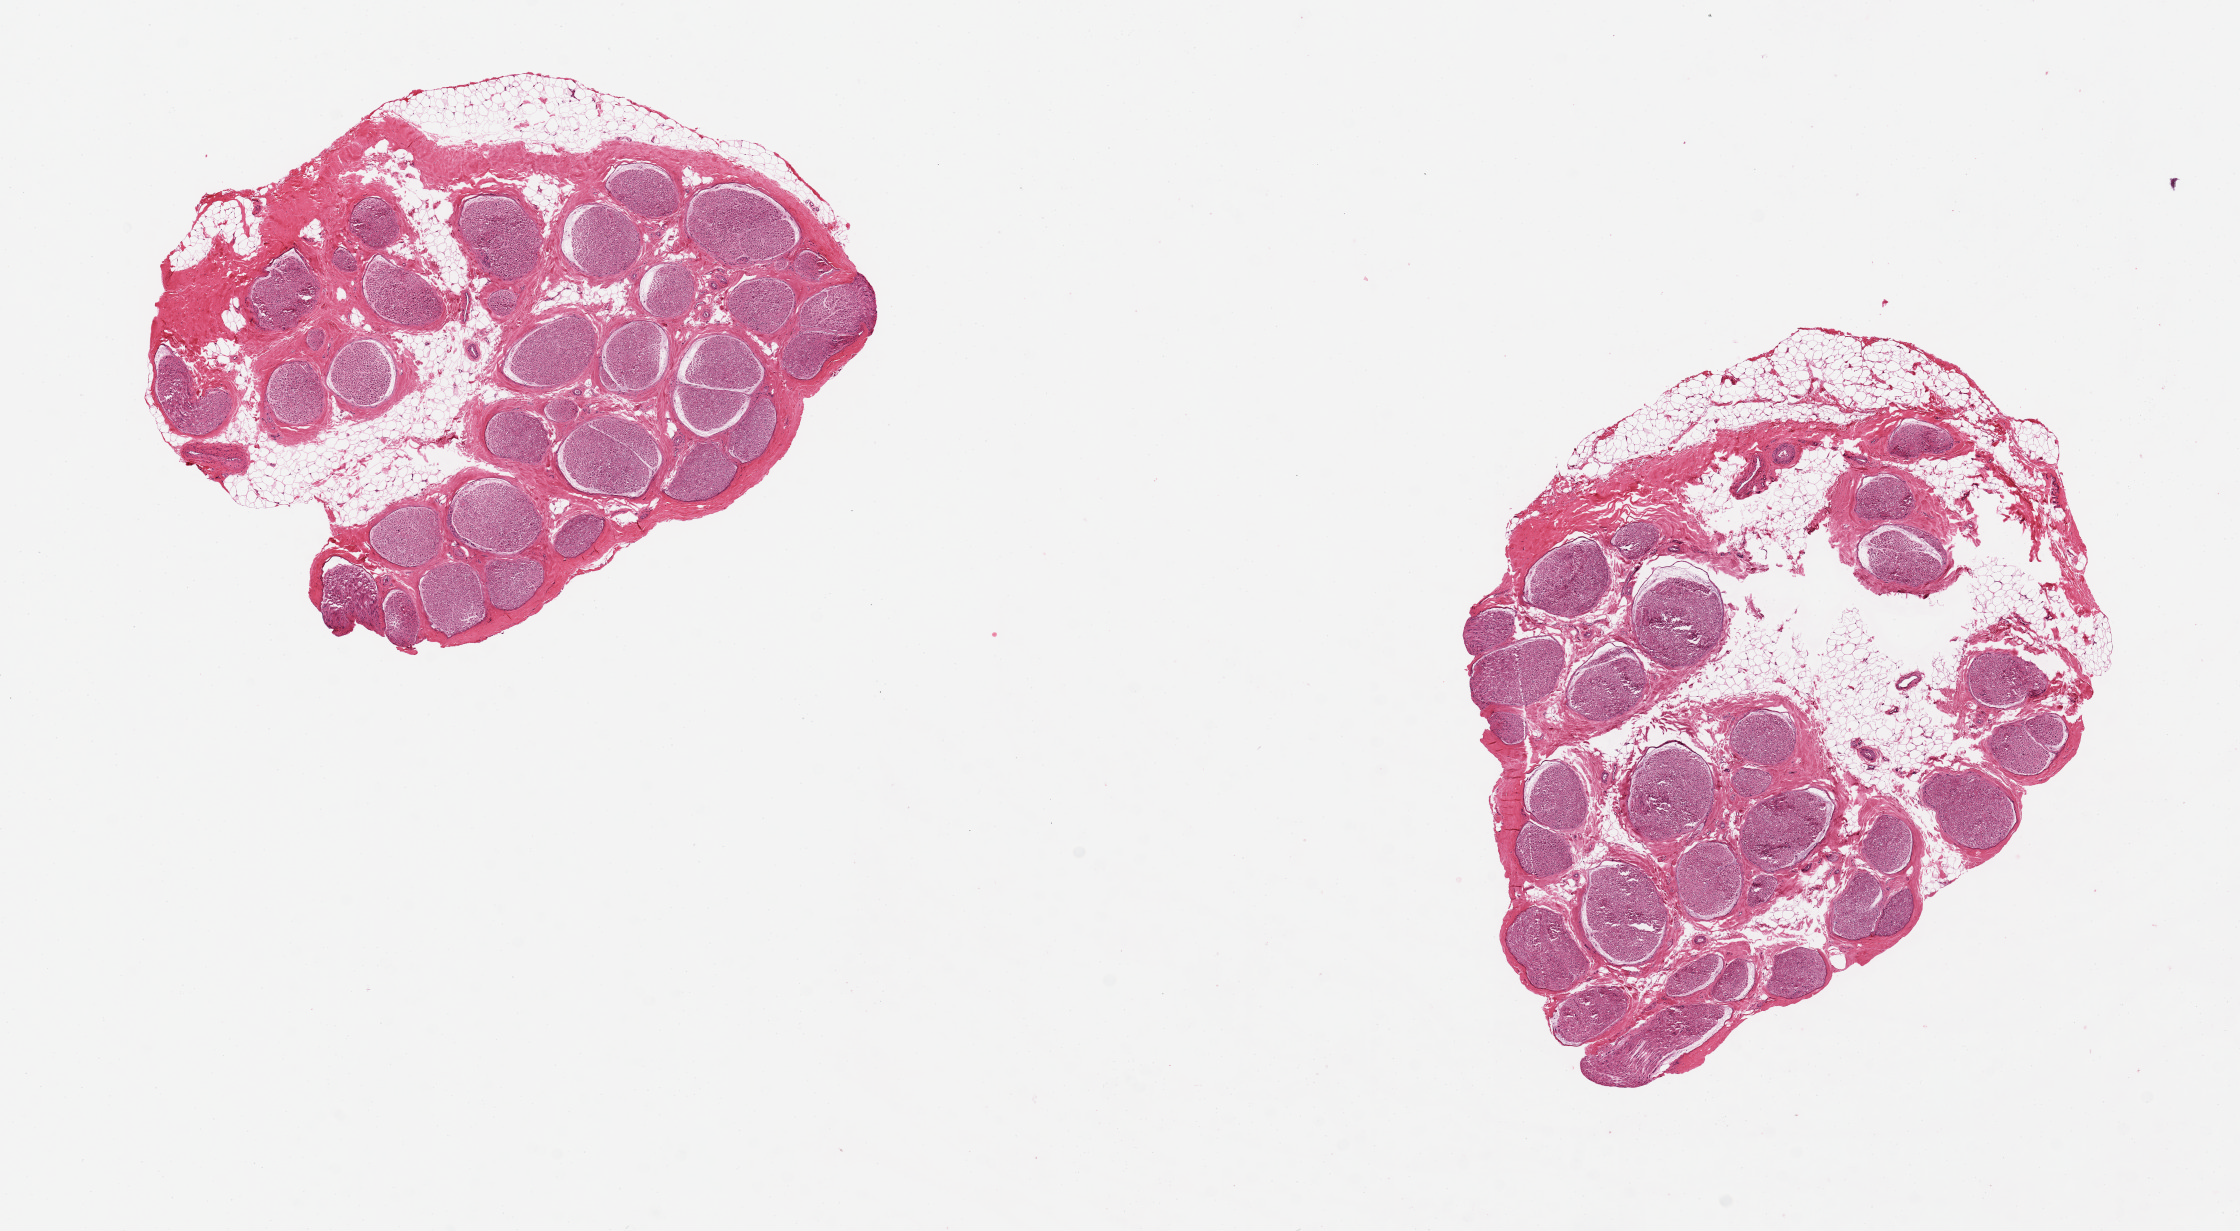
Hematoxylin and eosin (H&E) whole-slide image, brightfield, shown as a low-resolution overview of the whole scanned area (about 17.7 x 9.7 mm, slide scanned at 20x); PAXgene-fixed, paraffin-embedded tissue; sampled site (target tissue): tibial nerve; donor tissue sample. Donor sex: male.
Review note (as recorded): 5 x 4.2 mm specimen, 30% intermingled adipose tissue. Center of one aliquot is poorly fixed (adipose).